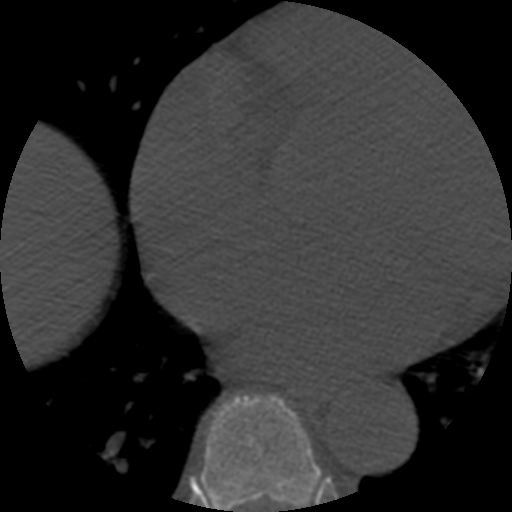
CT including the spine, one axial slice; position 325 of 508 along the scan axis; 120 kVp; bone window (W 1800 / L 400 HU); 1.25 mm slice thickness; 512 × 512 image matrix, field of view 160 × 160 mm. Patient age 57 years. Case-level facts recorded for this patient, not image findings: primary cancer: prostate.
Outlined on this slice (semi-automatically segmented with operator editing):
- T7 vertebra: bounding box (x1, y1, x2, y2) in pixels: (198, 394, 321, 512)